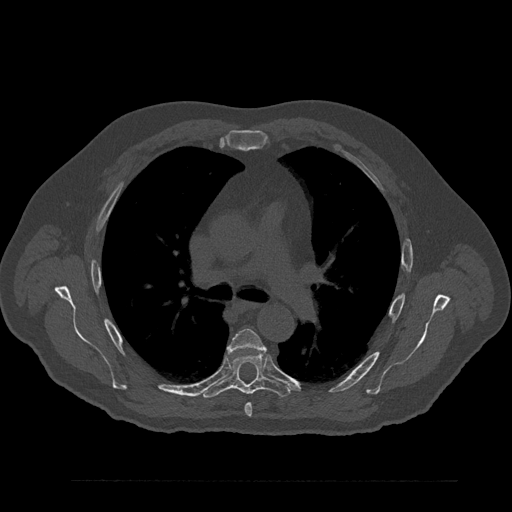
CT including the spine, one axial slice; position 572 of 797 along the scan axis; reconstruction kernel Br40s/3; 120 kVp; bone window (W 1800 / L 400 HU); 512 × 512 image matrix, field of view 430 × 430 mm. Male patient, age 61 years. Case-level facts recorded for this patient, not image findings: primary cancer: prostate.
Structures marked on this image (semi-automatically segmented with operator editing):
- T5 vertebra: box from (x=228, y=328) to (x=266, y=417) px
- T6 vertebra: (x=201, y=352)–(x=291, y=398)